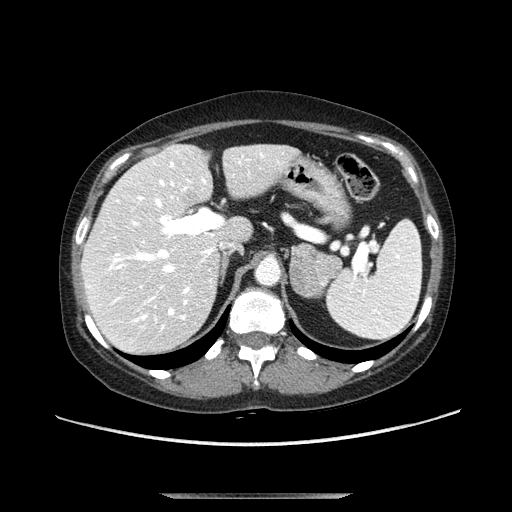
Contrast-enhanced abdominal CT, one axial slice; slice 72 of 107 in the series (ordered by position); soft-tissue window (W 400 / L 40 HU); 512 × 512 image matrix, field of view 380 × 380 mm. Female patient. From the clinical record (not read from this slice): diagnosis: adrenocortical carcinoma; tumour side: left adrenal; tumour size at pathology: 7.5 cm; Ki-67 index: 9 %; stage (as recorded): 3.
Outlined on this slice (semi-automatically segmented with operator editing):
- mass: bounding box <290,243,342,298> (left, top, right, bottom; pixels)